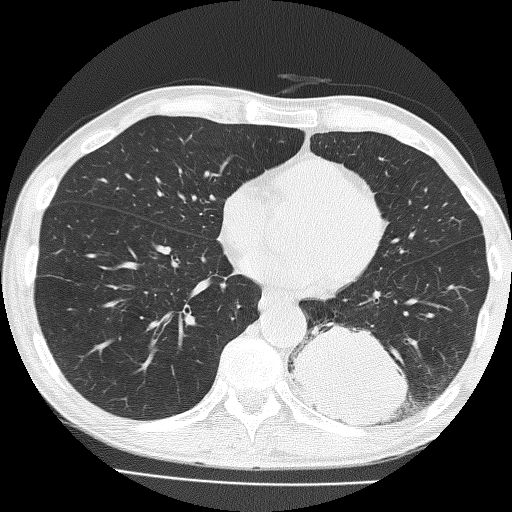
Axial slice from a low-dose chest CT screening exam, first (baseline) screen, lung window (W 1500 / L -600 HU), 2 mm slice thickness. Male participant, aged 58 years at enrolment. Current smoker at enrolment.
Expert-annotated lung lesion, box from (x=297, y=305) to (x=424, y=435) px. The screening reader recorded 2 non-calcified nodules or masses ≥4 mm on this exam (left lower lobe, left upper lobe); which of them this box marks is not recorded.